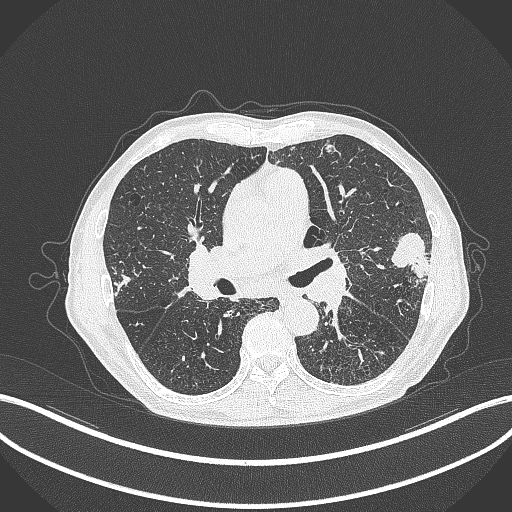
Chest CT, one axial slice; 120 kVp; lung window (W 1500 / L -600 HU); 1 mm slice thickness; 512 × 512 image matrix. Male patient, age 74 years. From the clinical record (not read from this slice): clinical TNM (as recorded): T2a N1 M0.
Annotated regions visible in this slice (bounding box drawn by a radiologist):
- lung tumour (recorded histology: adenocarcinoma): box from (x=387, y=226) to (x=433, y=277) px